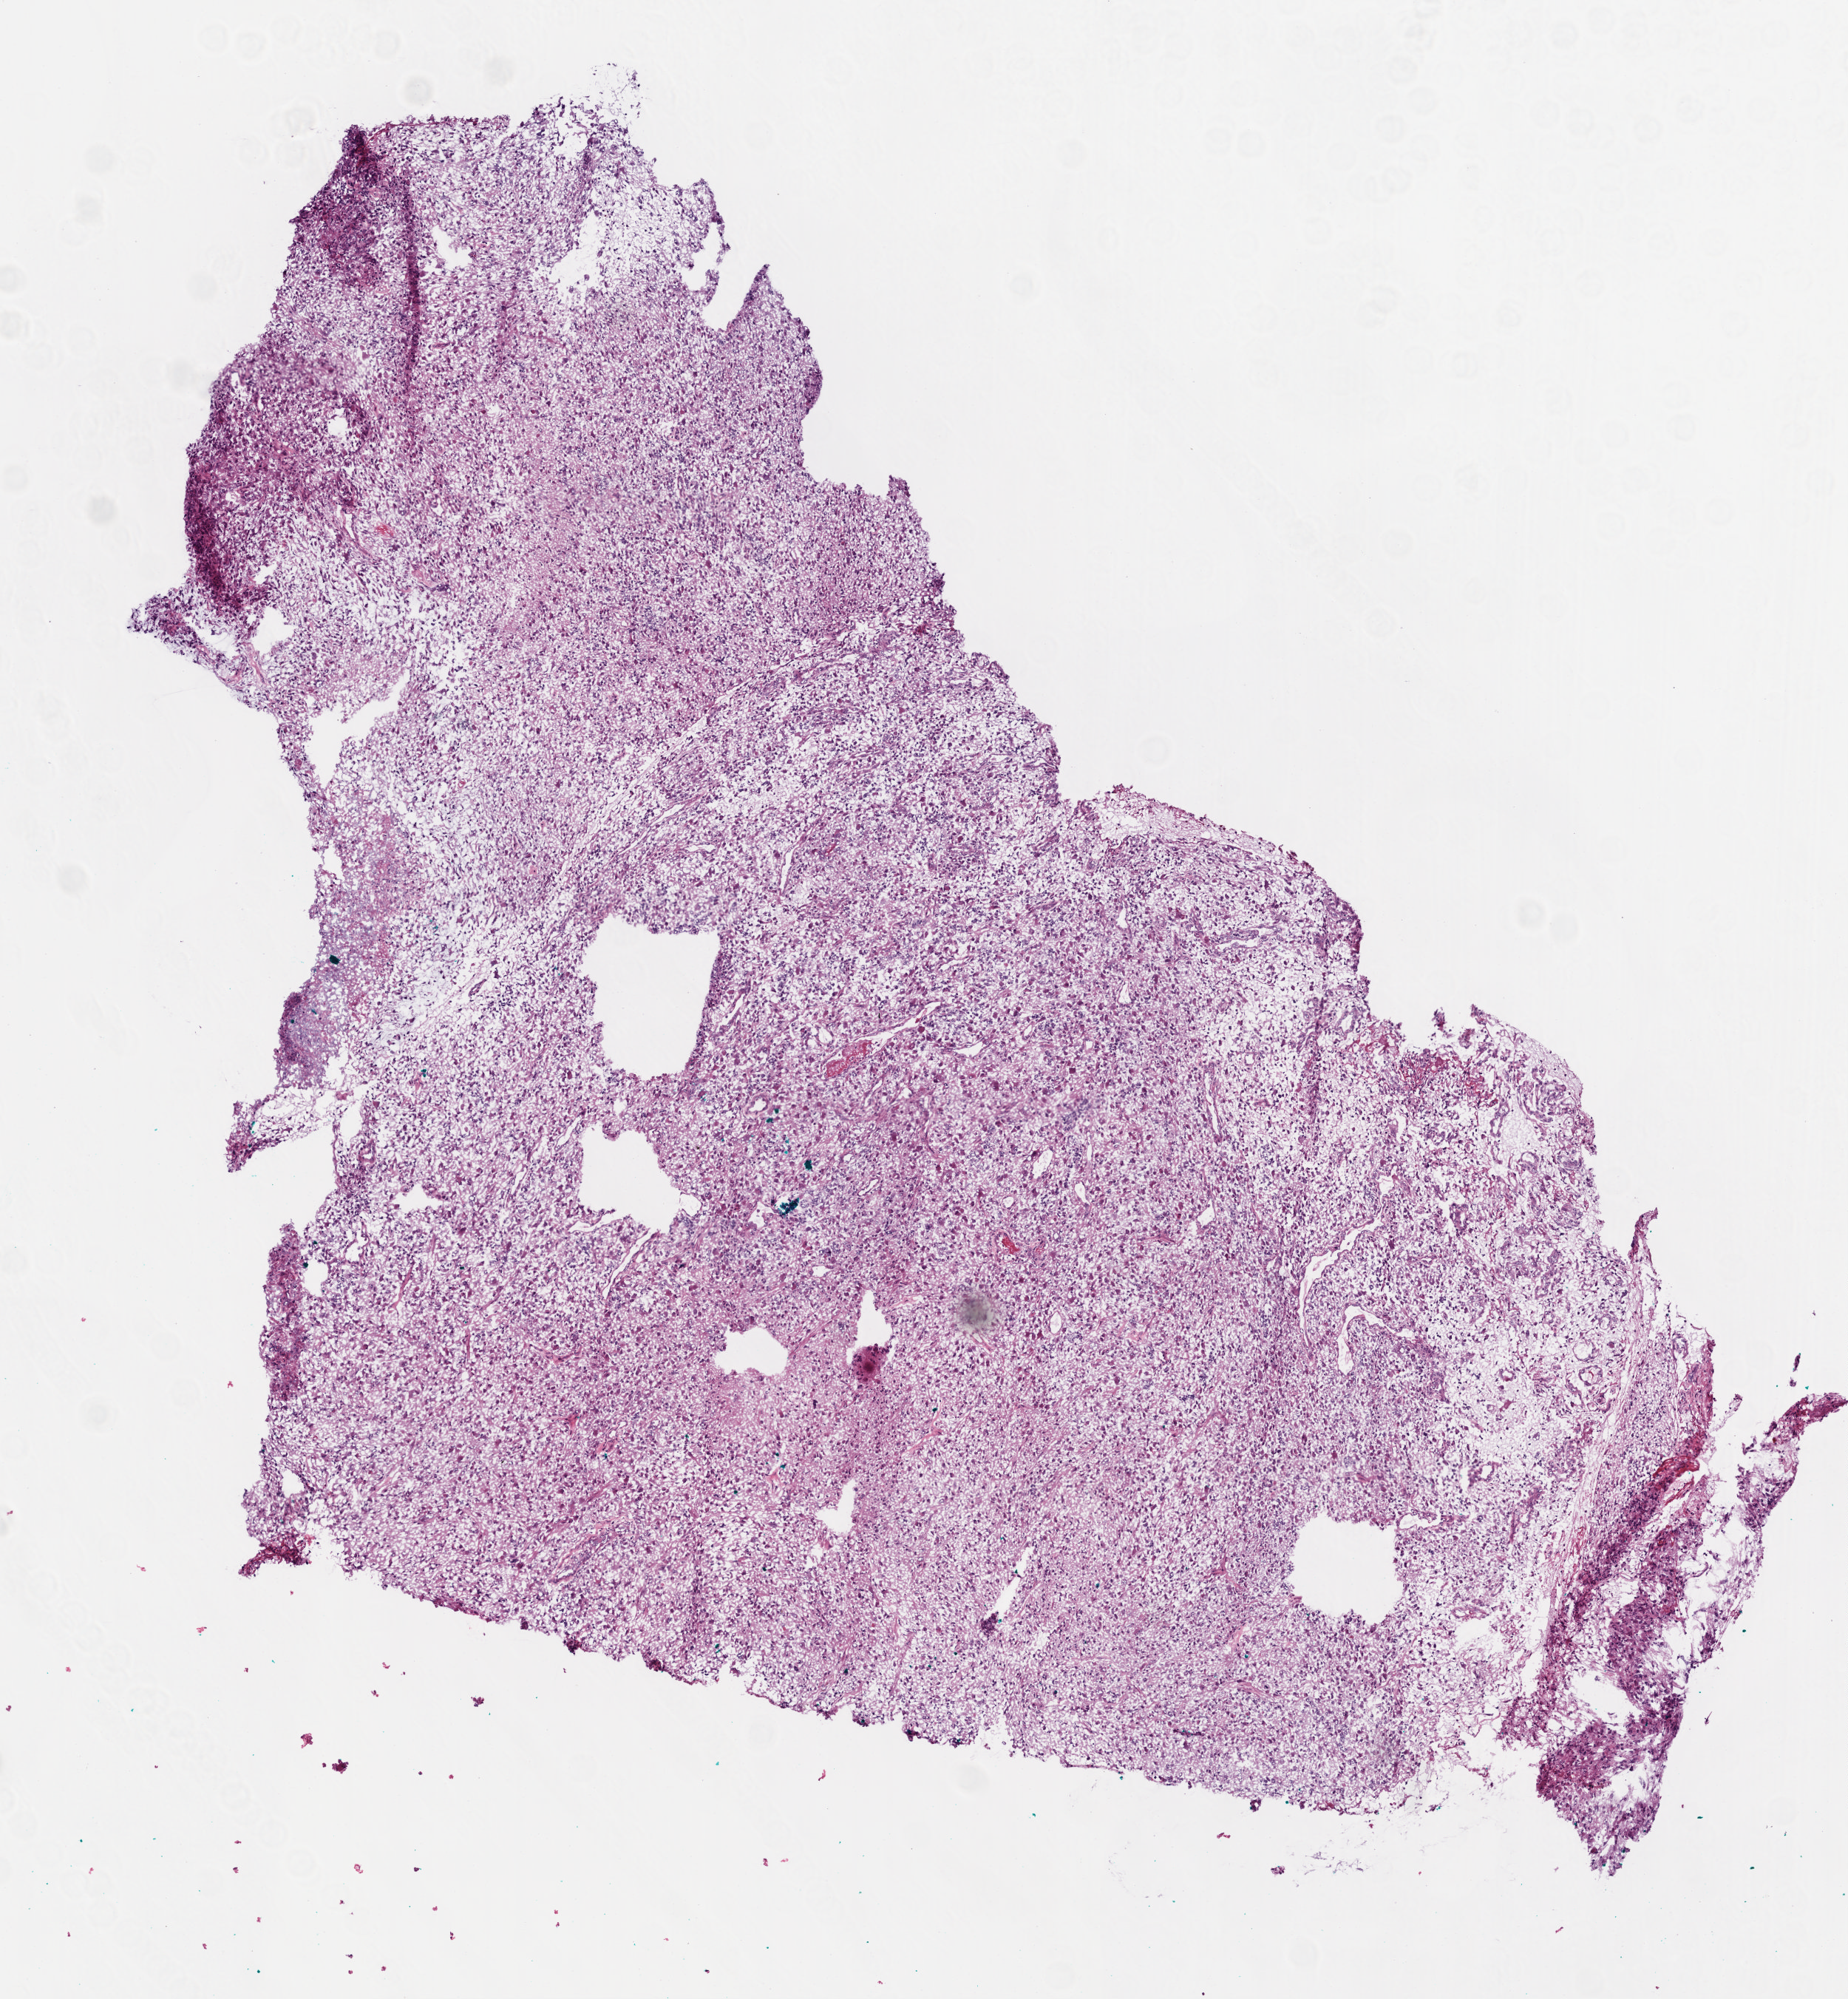
Hematoxylin and eosin (H&E) stained whole-slide image, a low-resolution overview of the entire scanned area, about 5.0 x 5.4 mm (from a 20x scan). Frozen section from the top of the tissue portion. Brain, primary tumour sample. Female patient; age at initial diagnosis 47 years. Pathologist review of this section (percent, as recorded): tumour cells 90%, tumour nuclei 70%, normal cells 0%, stromal cells 0%, necrosis 10%.
• pathologic diagnosis: Glioblastoma